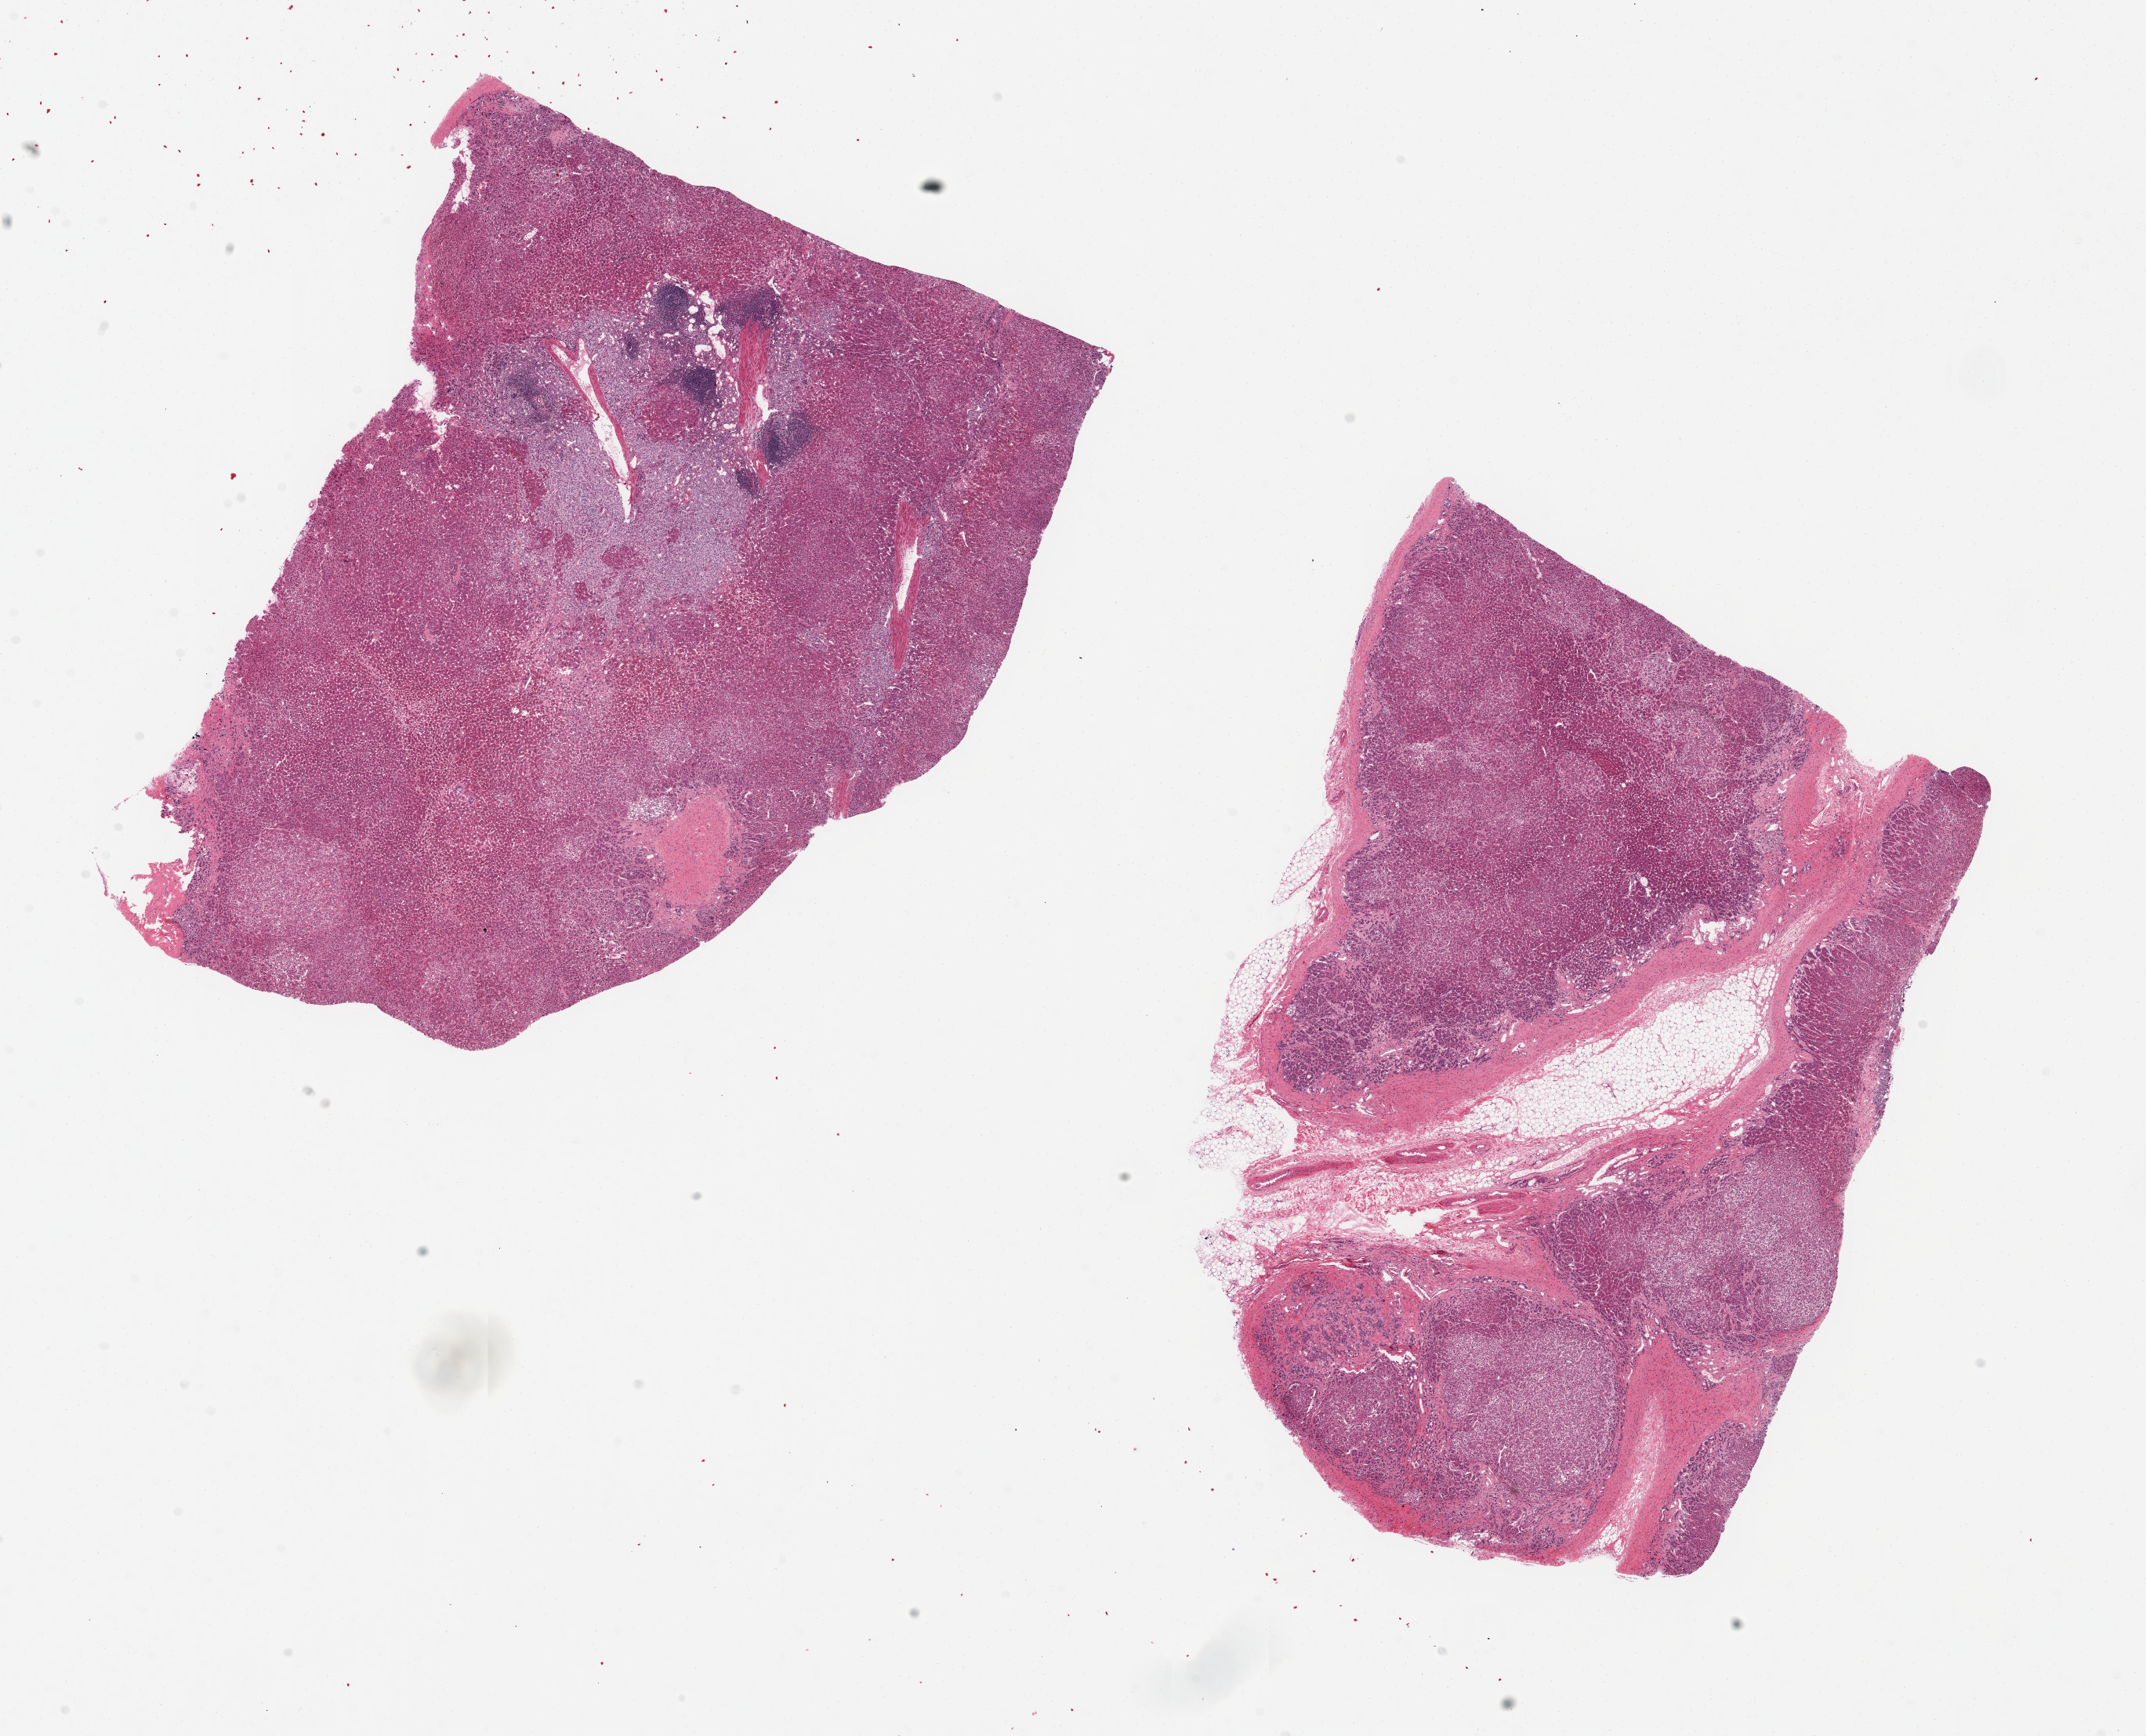
Whole-slide image, H&E stain, brightfield — shown as a low-resolution overview of the whole scanned area (about 21.7 x 17.5 mm); PAXgene-fixed, paraffin-embedded tissue; target tissue: adrenal gland; donor tissue sample. Female donor.
* reviewer comment on this tissue sample: 2 aliquots, ~9x7mm. Foci of chronic inflammation